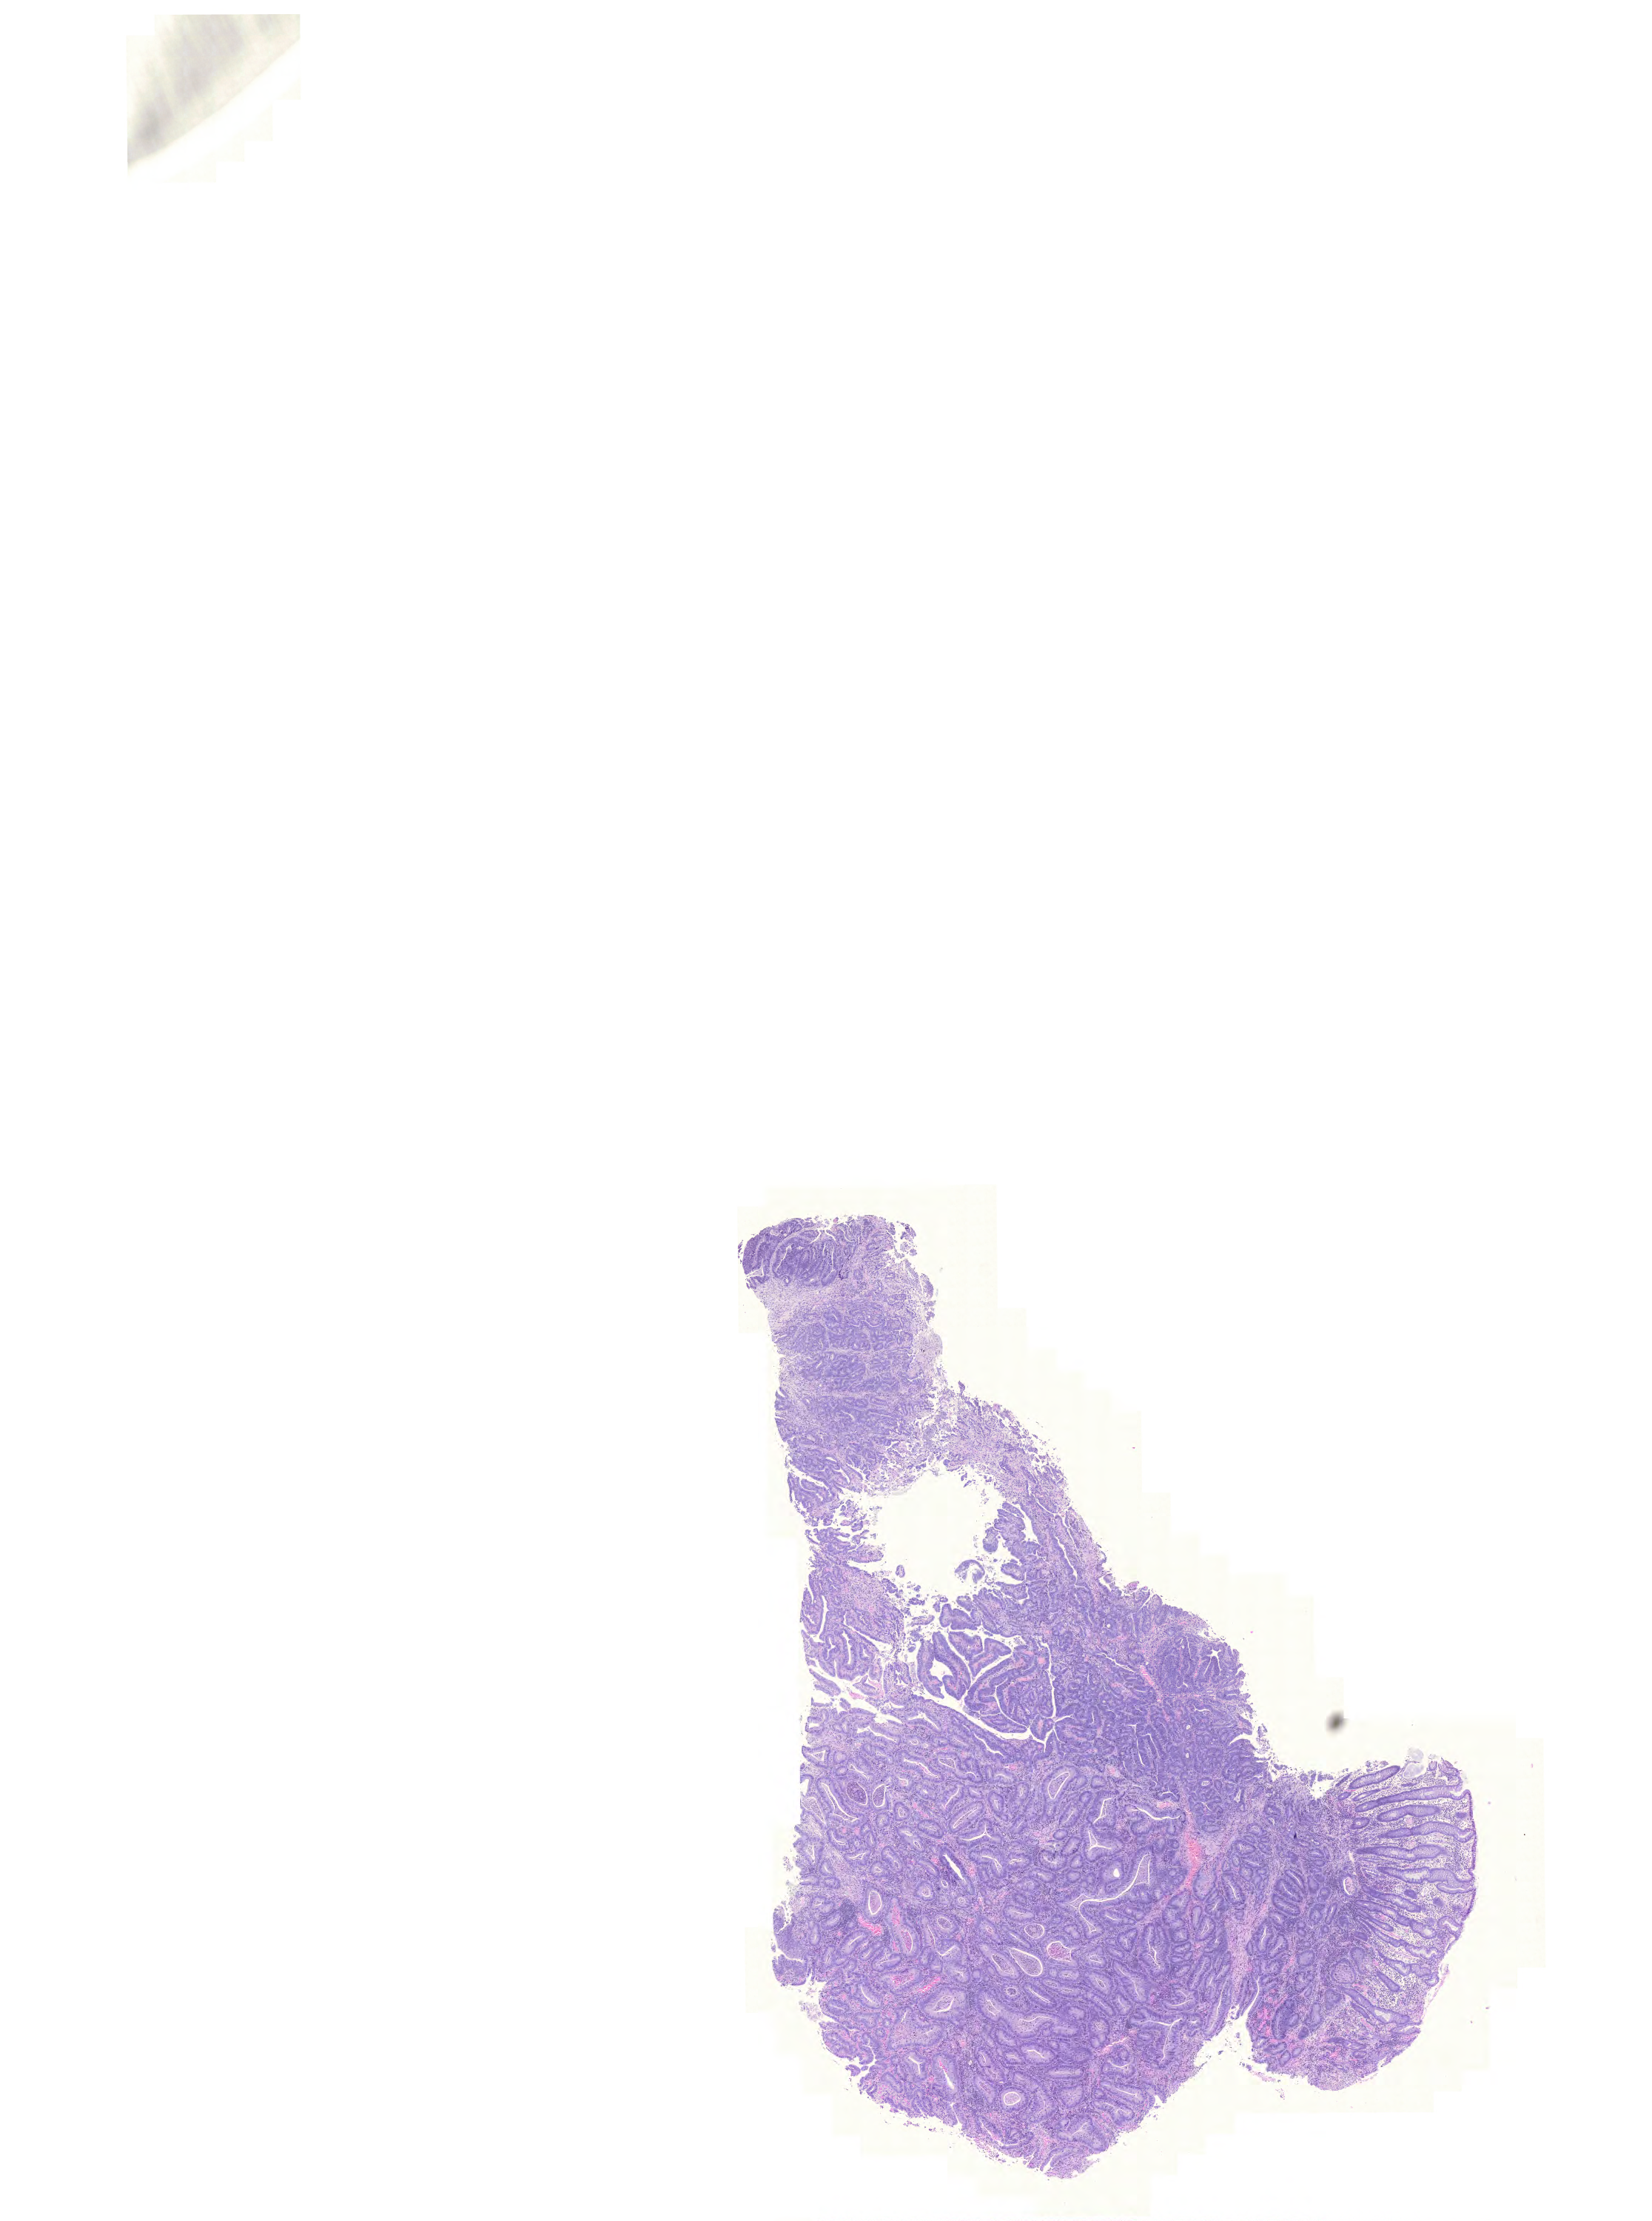
Digitized H&E tissue section (whole slide) — whole scanned area (about 16.6 x 22.3 mm, acquisition: 20x scan) shown as a low-resolution overview, formalin-fixed paraffin-embedded (FFPE) diagnostic section, primary tumour sample from the colon. Patient: male, age at initial diagnosis 82 years.
* diagnosis: Adenocarcinoma, NOS
* TNM: T3 N0 M0
* AJCC pathologic stage: IIA (6th edition)
* lymph nodes positive (case pathology): 0 of 16 examined